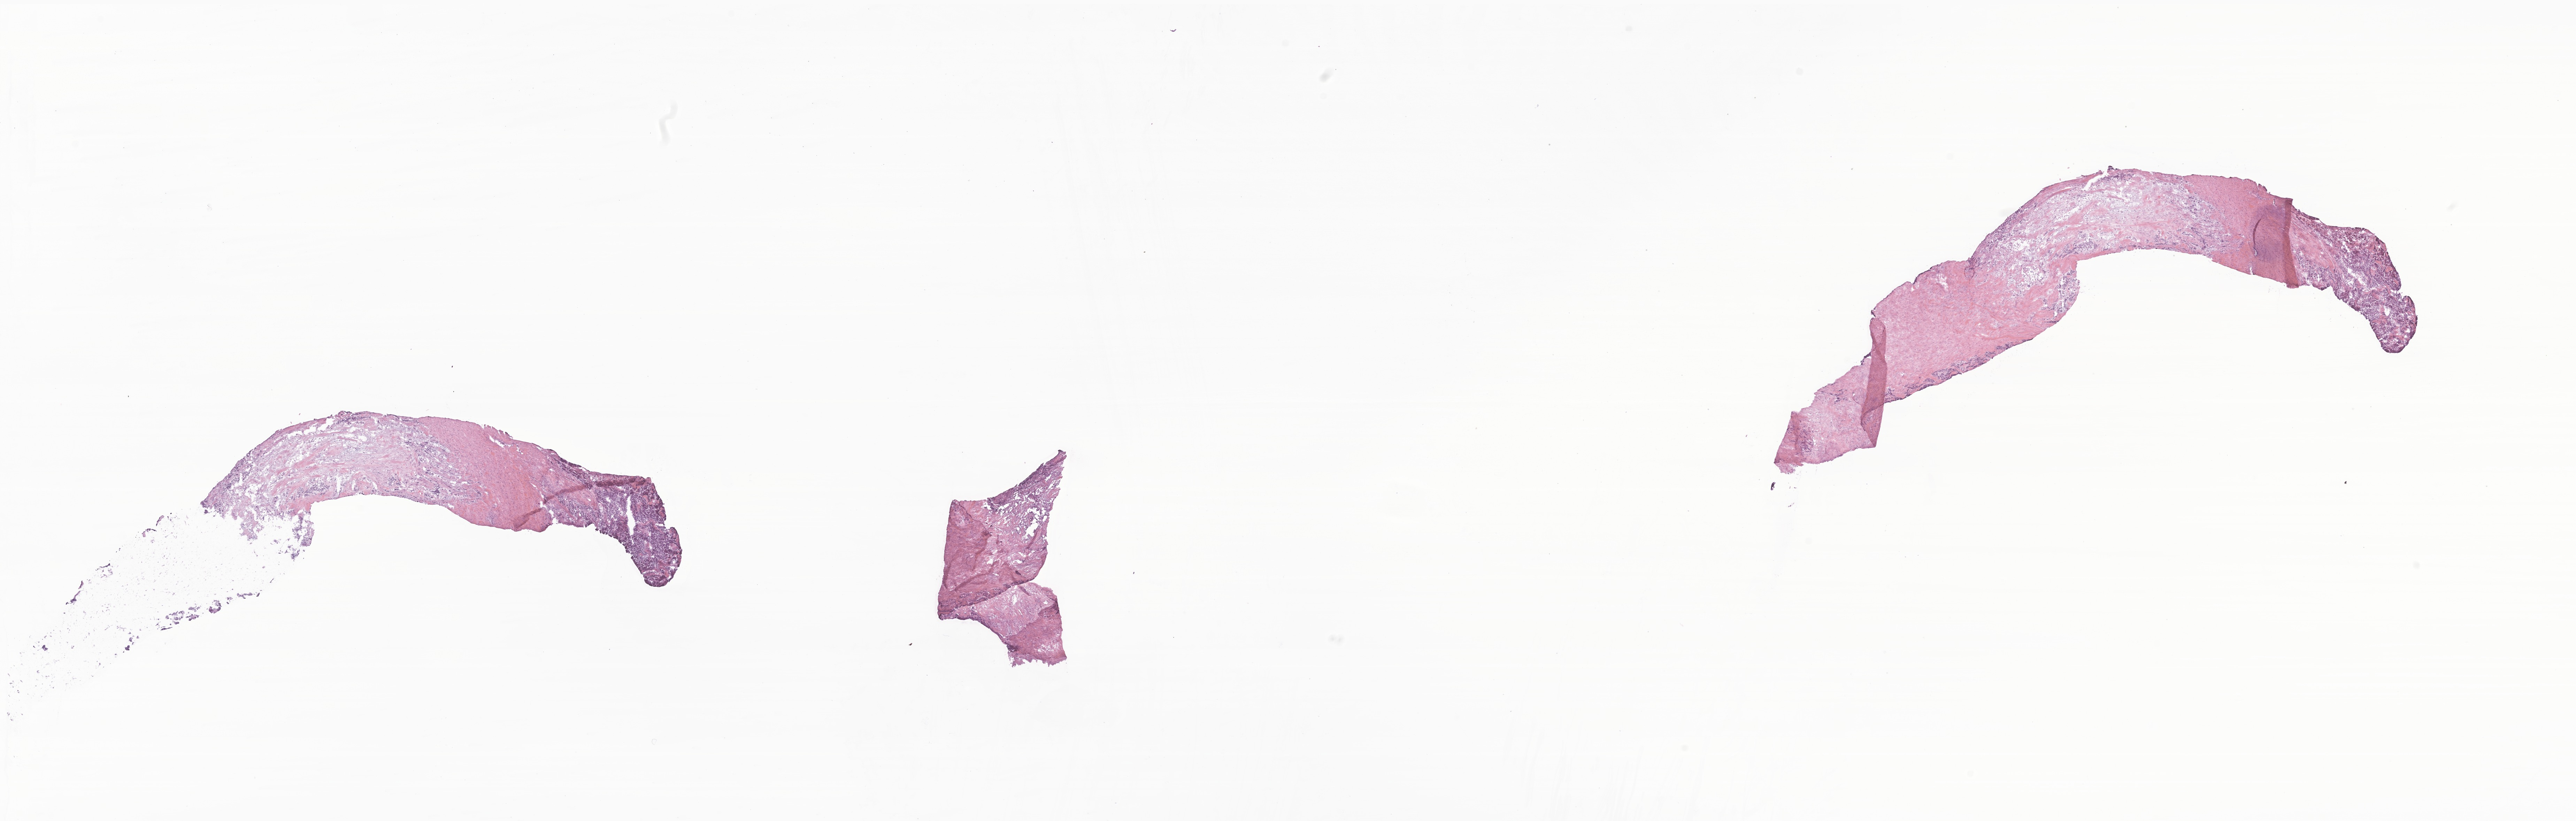
Digitized hematoxylin and eosin (H&E)-stained section of tumor tissue from the pelvis — low-resolution overview of the scanned area, about 31.2 x 9.9 mm. Frozen section (OCT-embedded). Patient: female, age 199 months (16 years 7 months).
* recorded diagnosis: Alveolar rhabdomyosarcoma